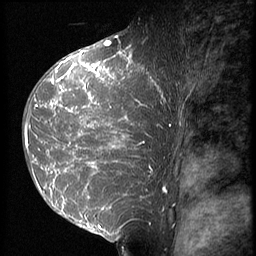
Breast MRI (dynamic contrast-enhanced), one sagittal slice; position 36 of 64 along the scan axis; 3 images stored at this slice position (order not interpretable as contrast timing); 1.5 T; TE 4.2 ms, TR 9 ms; 256 × 256 image matrix, field of view 180 × 180 mm. Patient: female, 39 years. Case-level facts recorded for this patient, not image findings: setting: breast cancer imaged before/during neoadjuvant chemotherapy; receptor status: HER2-positive.
Annotated regions visible in this slice (semi-automatic segmentation, software-assisted and operator-edited):
- analysis volume of interest (the breast-tissue region the enhancement analysis was run in; not a lesion): bounding box [x1, y1, x2, y2] px = [23, 47, 163, 239]
- tumour enhancement mask (voxels above the 140 % enhancement threshold inside the analysis volume of interest): [25, 50, 160, 228]